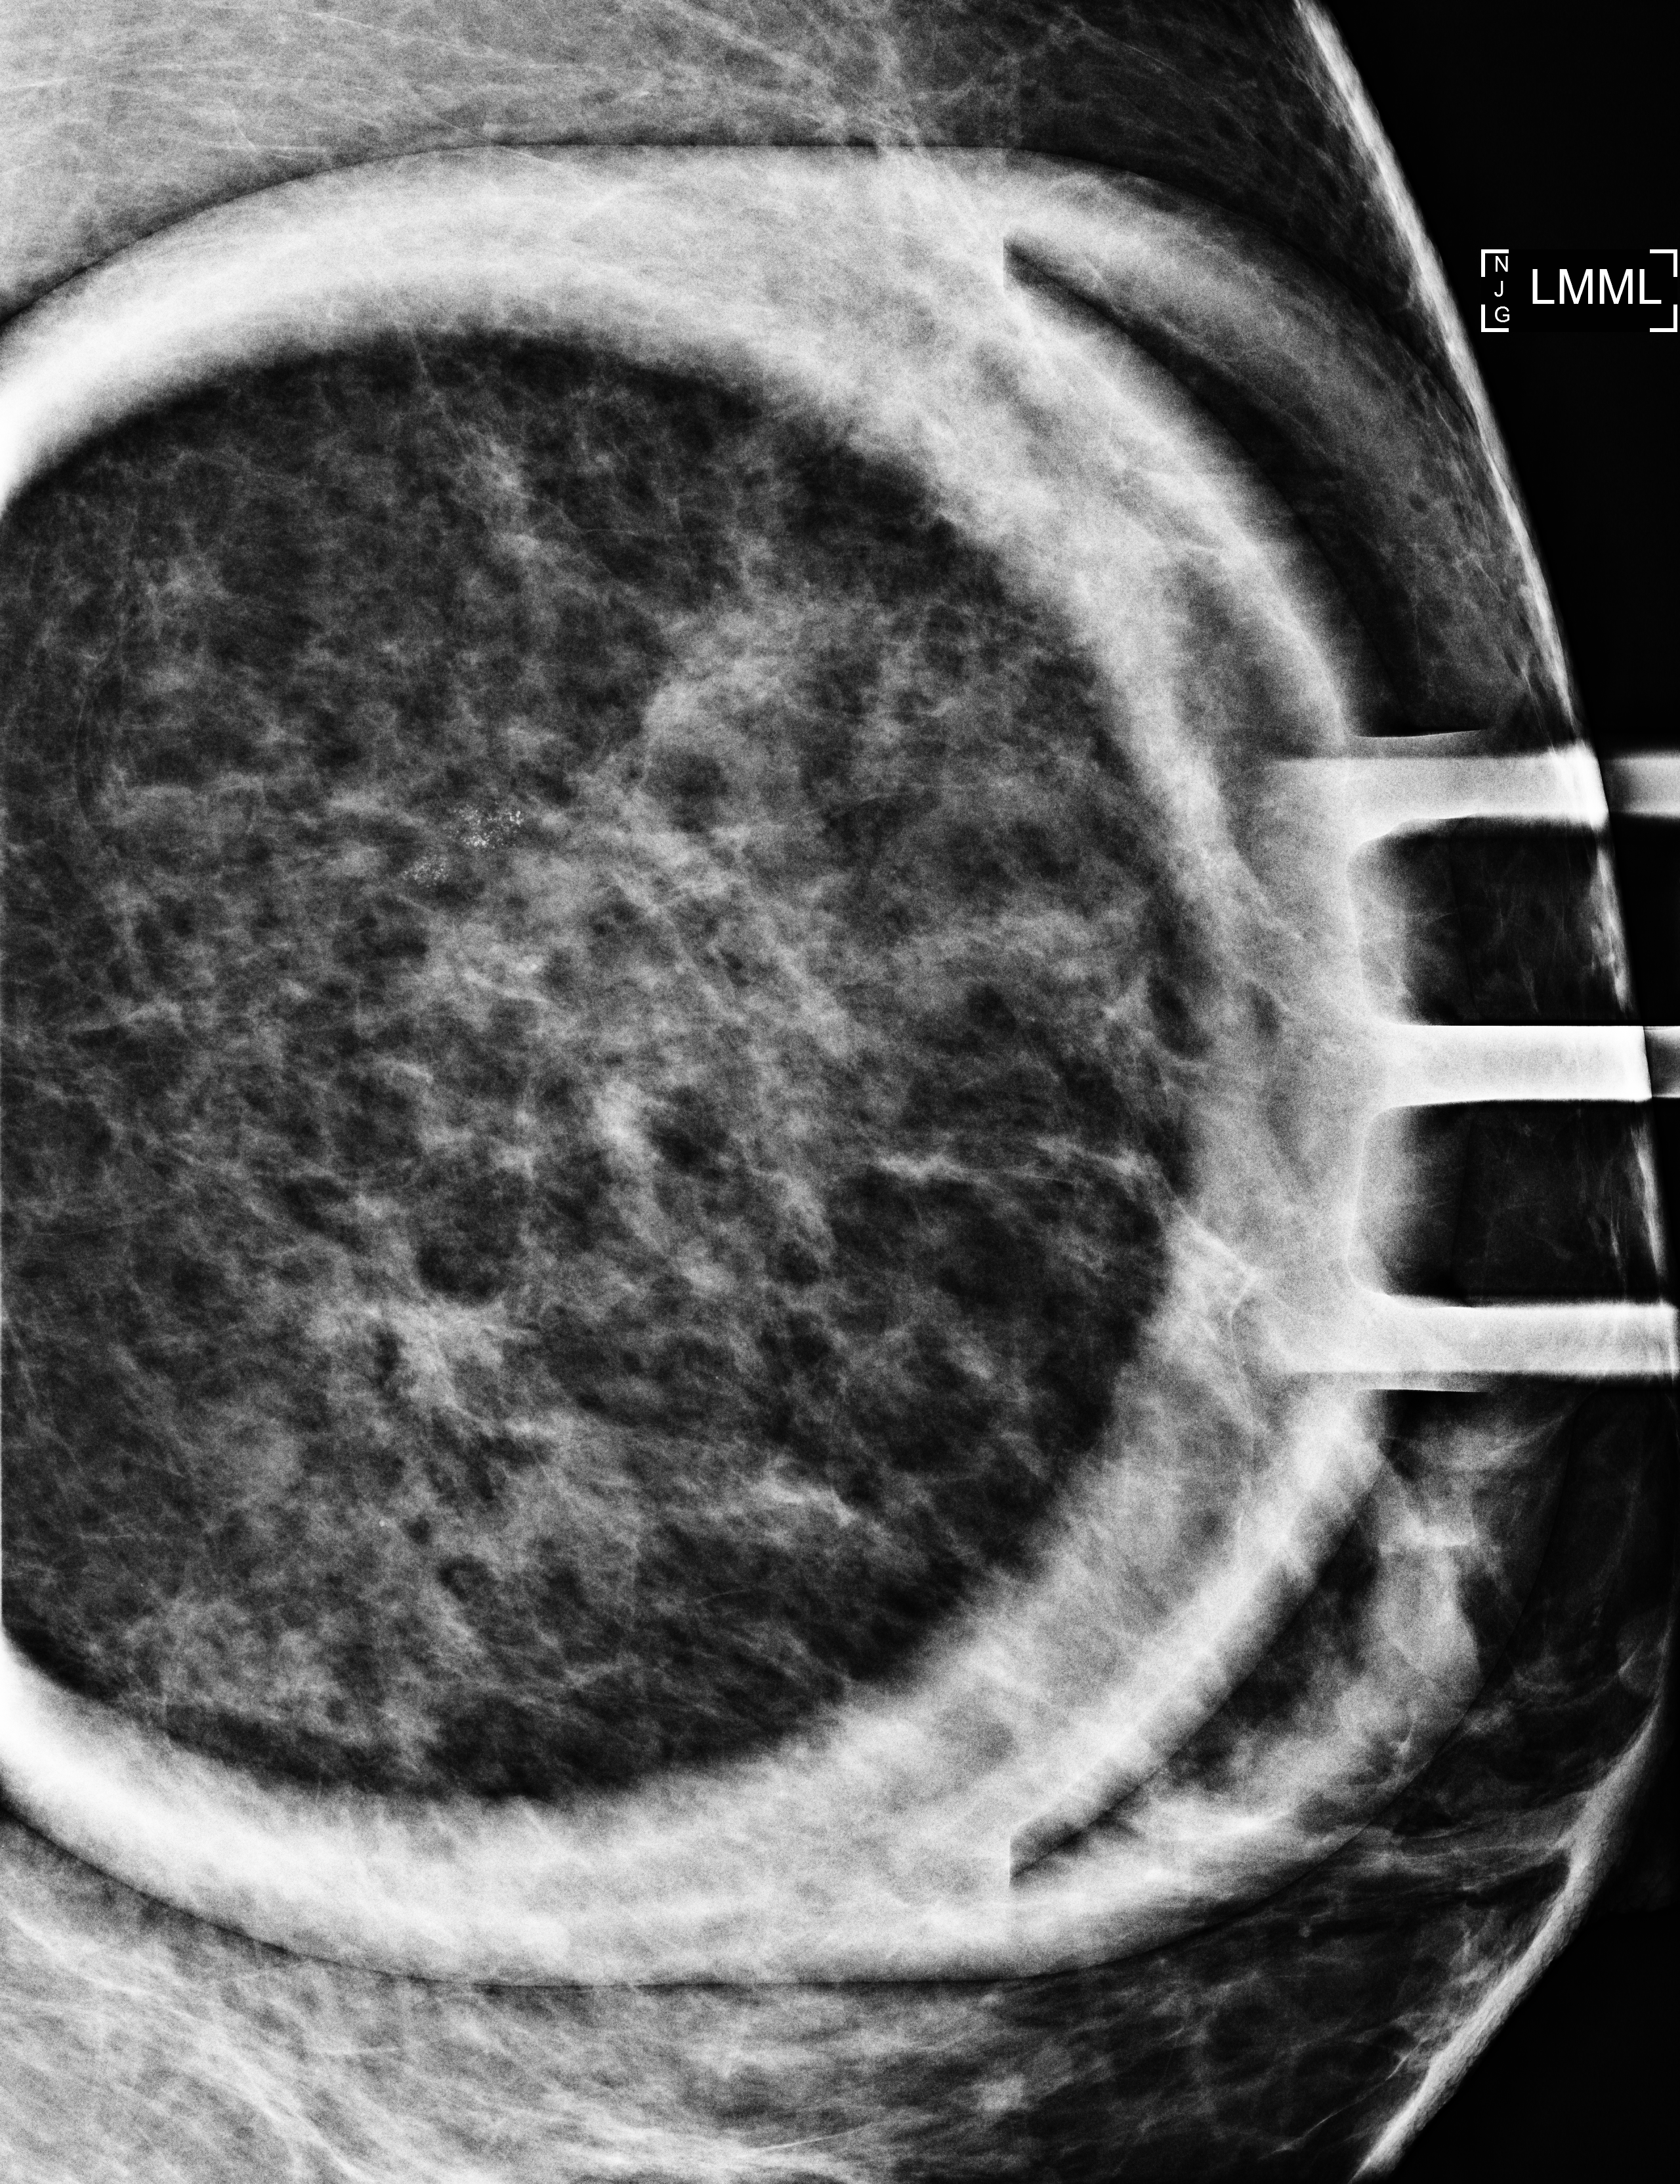
Additional work-up view, system: Selenia Dimensions. Female patient, age 71 years.
Image type: full-field digital mammogram. Breast: left. Projection: mediolateral (ML) view, magnification.